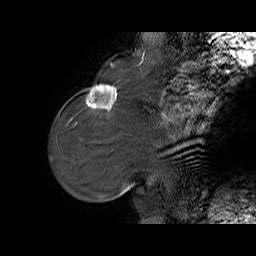
Breast MRI (dynamic contrast-enhanced), one sagittal slice; dynamic contrast-enhanced series, time point 2 of 6 at this slice position (early post-contrast); 1.5 T; TE 5.7 ms, TR 32.9 ms; 256 × 256 image matrix, field of view 230 × 230 mm. Female patient. From the clinical record (not read from this slice): setting: breast cancer imaged before/during neoadjuvant chemotherapy; receptor status: HER2-positive.
Outlined on this slice (semi-automatically segmented with operator editing):
- analysis volume of interest (the breast-tissue region the enhancement analysis was run in; not a lesion): bounding box [x1, y1, x2, y2] px = [76, 77, 125, 128]
- tumour enhancement mask (voxels above the 100 % enhancement threshold inside the analysis volume of interest): [86, 84, 117, 109]